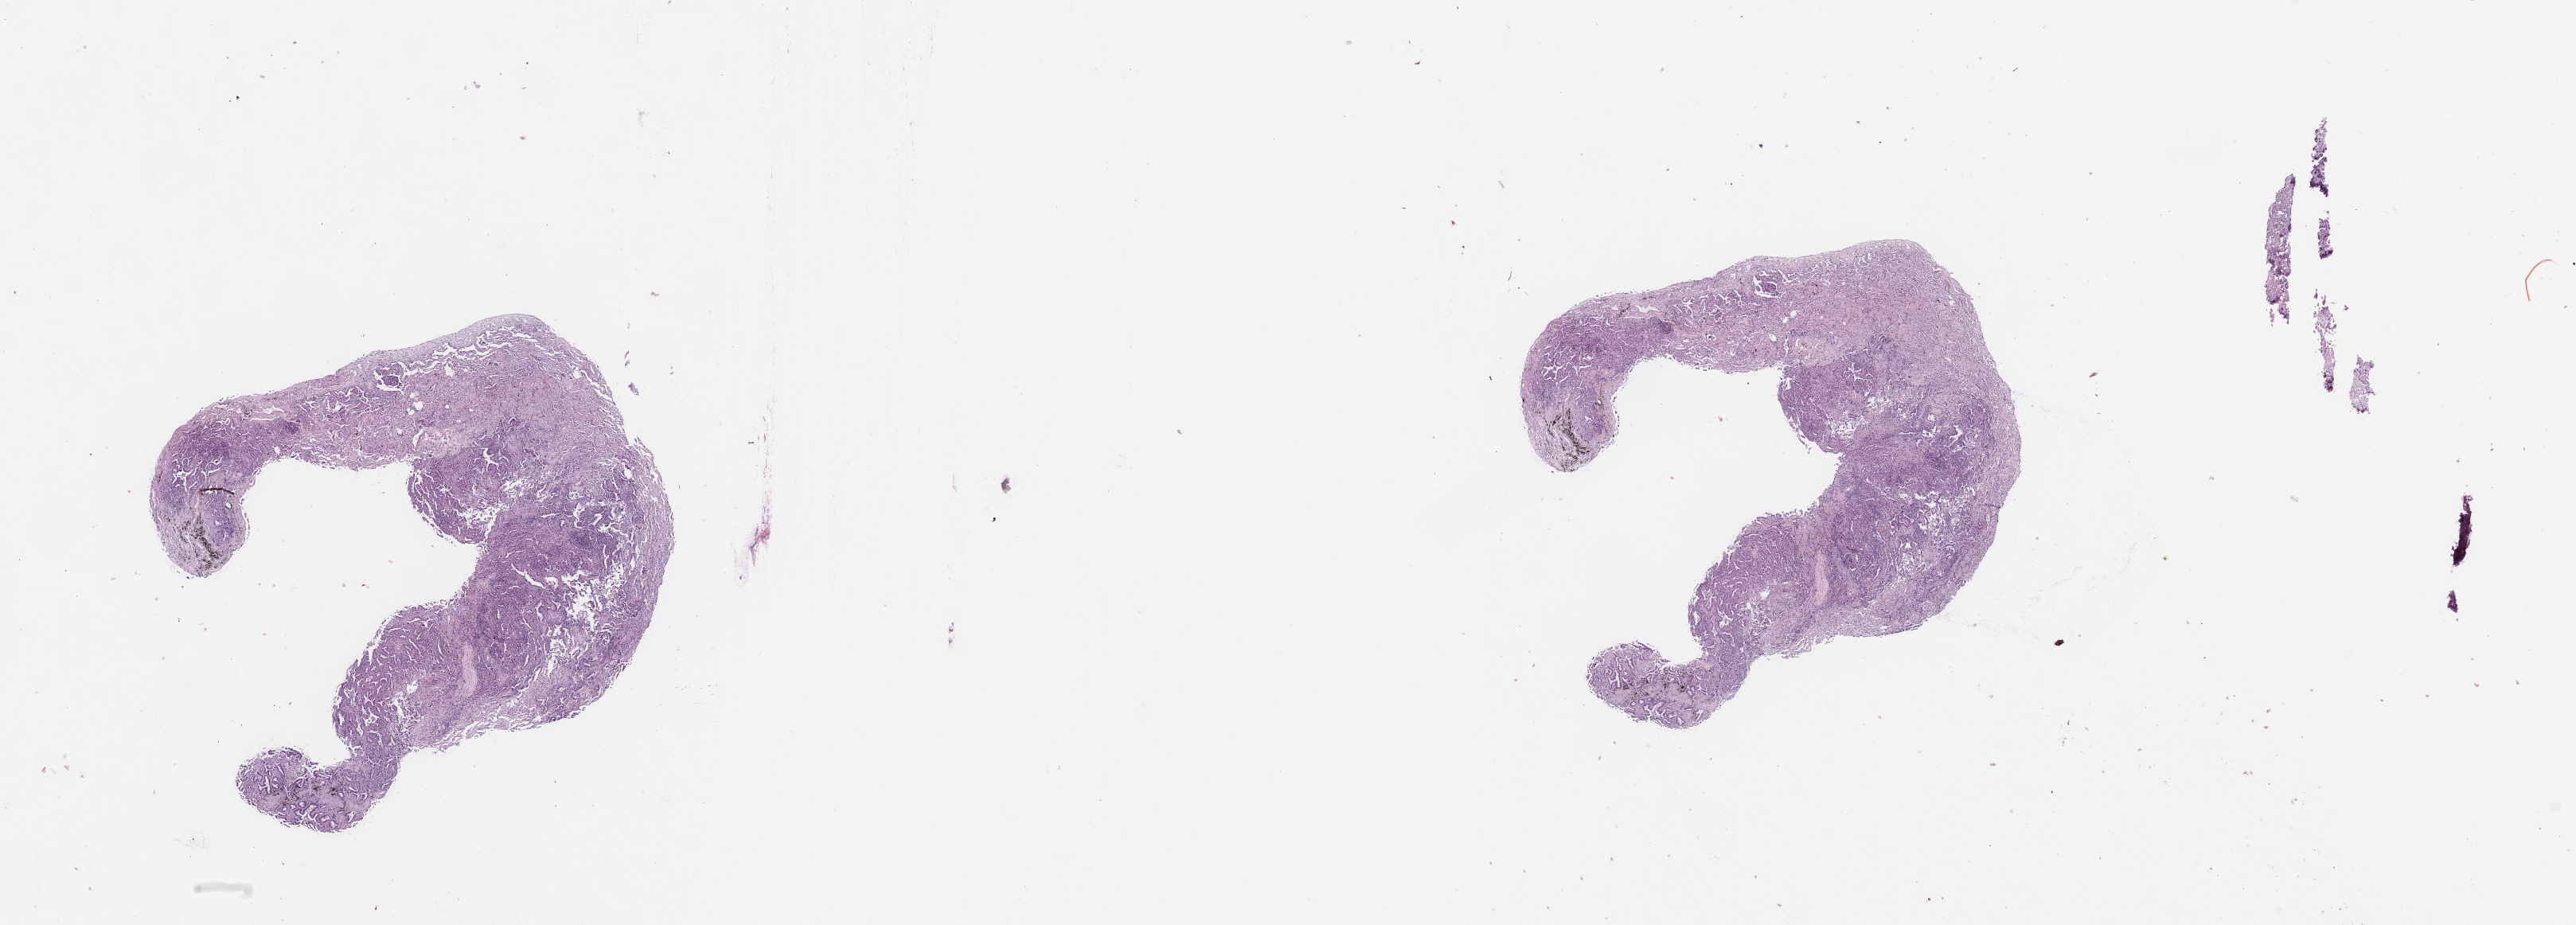
Whole-slide histology image, H&E-stained — whole scanned area (about 25.6 x 9.2 mm, from a 20x scan) shown as a low-resolution overview, lung, tumour tissue. Male, 77 y/o. Histologic grade: G2 (moderately differentiated).
• AJCC pathologic stage: IIIA
• diagnosis: Adenocarcinoma, NOS